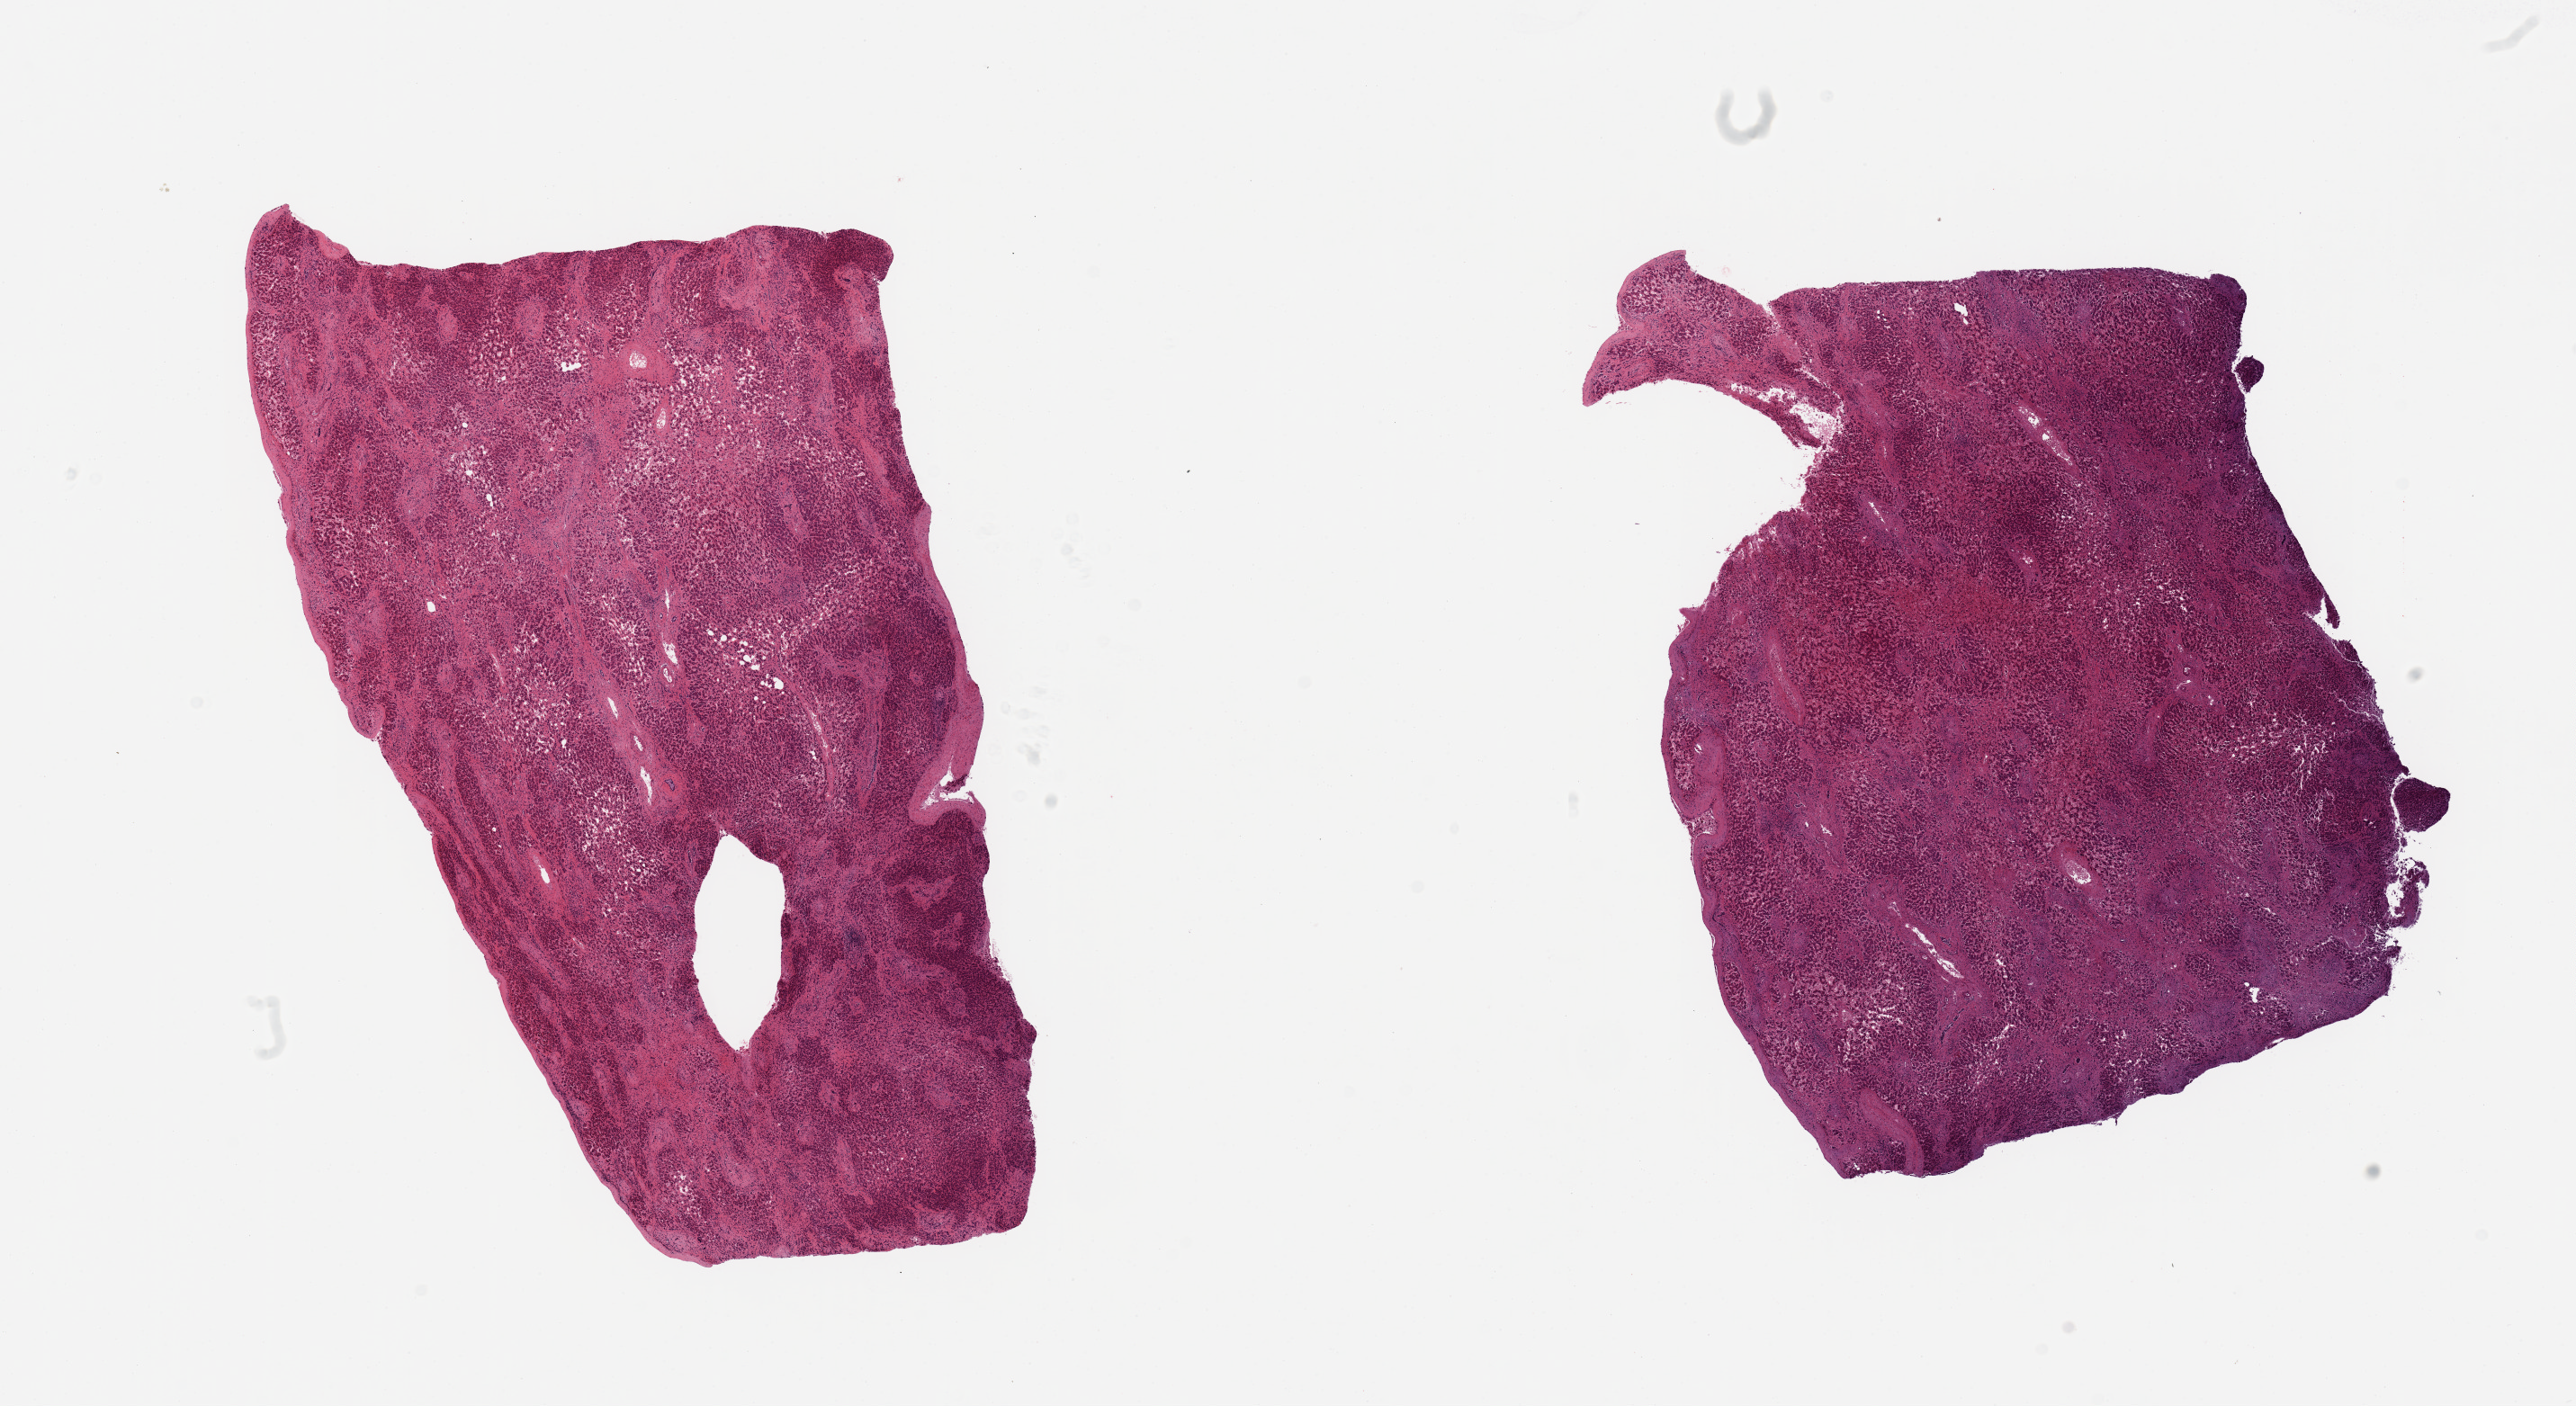
H&E whole-slide image, low-resolution overview of the scanned area, about 22.6 x 12.4 mm (acquisition: 20x scan); PAXgene-fixed, paraffin-embedded tissue; sampled site (target tissue): liver; donor tissue sample.
* reviewer comment on this tissue sample: 2 pieces; severe fibrosis without nodule formation consistent with cardiac cirrhosis, possible venous outflow obstruction